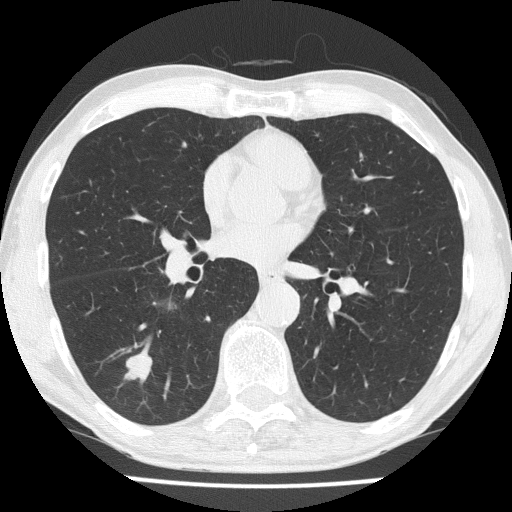
Low-dose screening chest CT, one axial slice; slice 82 of 186 in the series (ordered by position); reconstruction kernel FC51; 120 kVp; lung window (W 1500 / L -600 HU); 2 mm slice thickness; 512 × 512 image matrix, field of view 328 × 328 mm.
Outlined on this slice (outlined manually by an expert reader):
- lesion 1 (tumor, lower lobe of right lung): bounding box (x1, y1, x2, y2) in pixels: (125, 349, 152, 382)